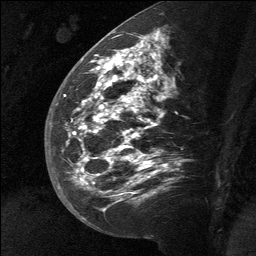
Breast MRI (dynamic contrast-enhanced), one sagittal slice; dynamic contrast-enhanced study with each time point stored as its own series, time point 2 of 3 at this slice position (early post-contrast, ordered by acquisition time); 1.5 T; TE 4.8 ms, TR 27 ms; 2 mm slice thickness; 256 × 256 image matrix. Patient: female, 39 years. From the clinical record (not read from this slice): setting: breast cancer imaged before/during neoadjuvant chemotherapy; receptor status: HER2-positive.
Structures marked on this image (semi-automatic segmentation, software-assisted and operator-edited):
- analysis volume of interest (the breast-tissue region the enhancement analysis was run in; not a lesion): bounding box <58,40,166,217> (left, top, right, bottom; pixels)
- tumour enhancement mask (voxels above the 90 % enhancement threshold inside the analysis volume of interest): <72,40,155,197>